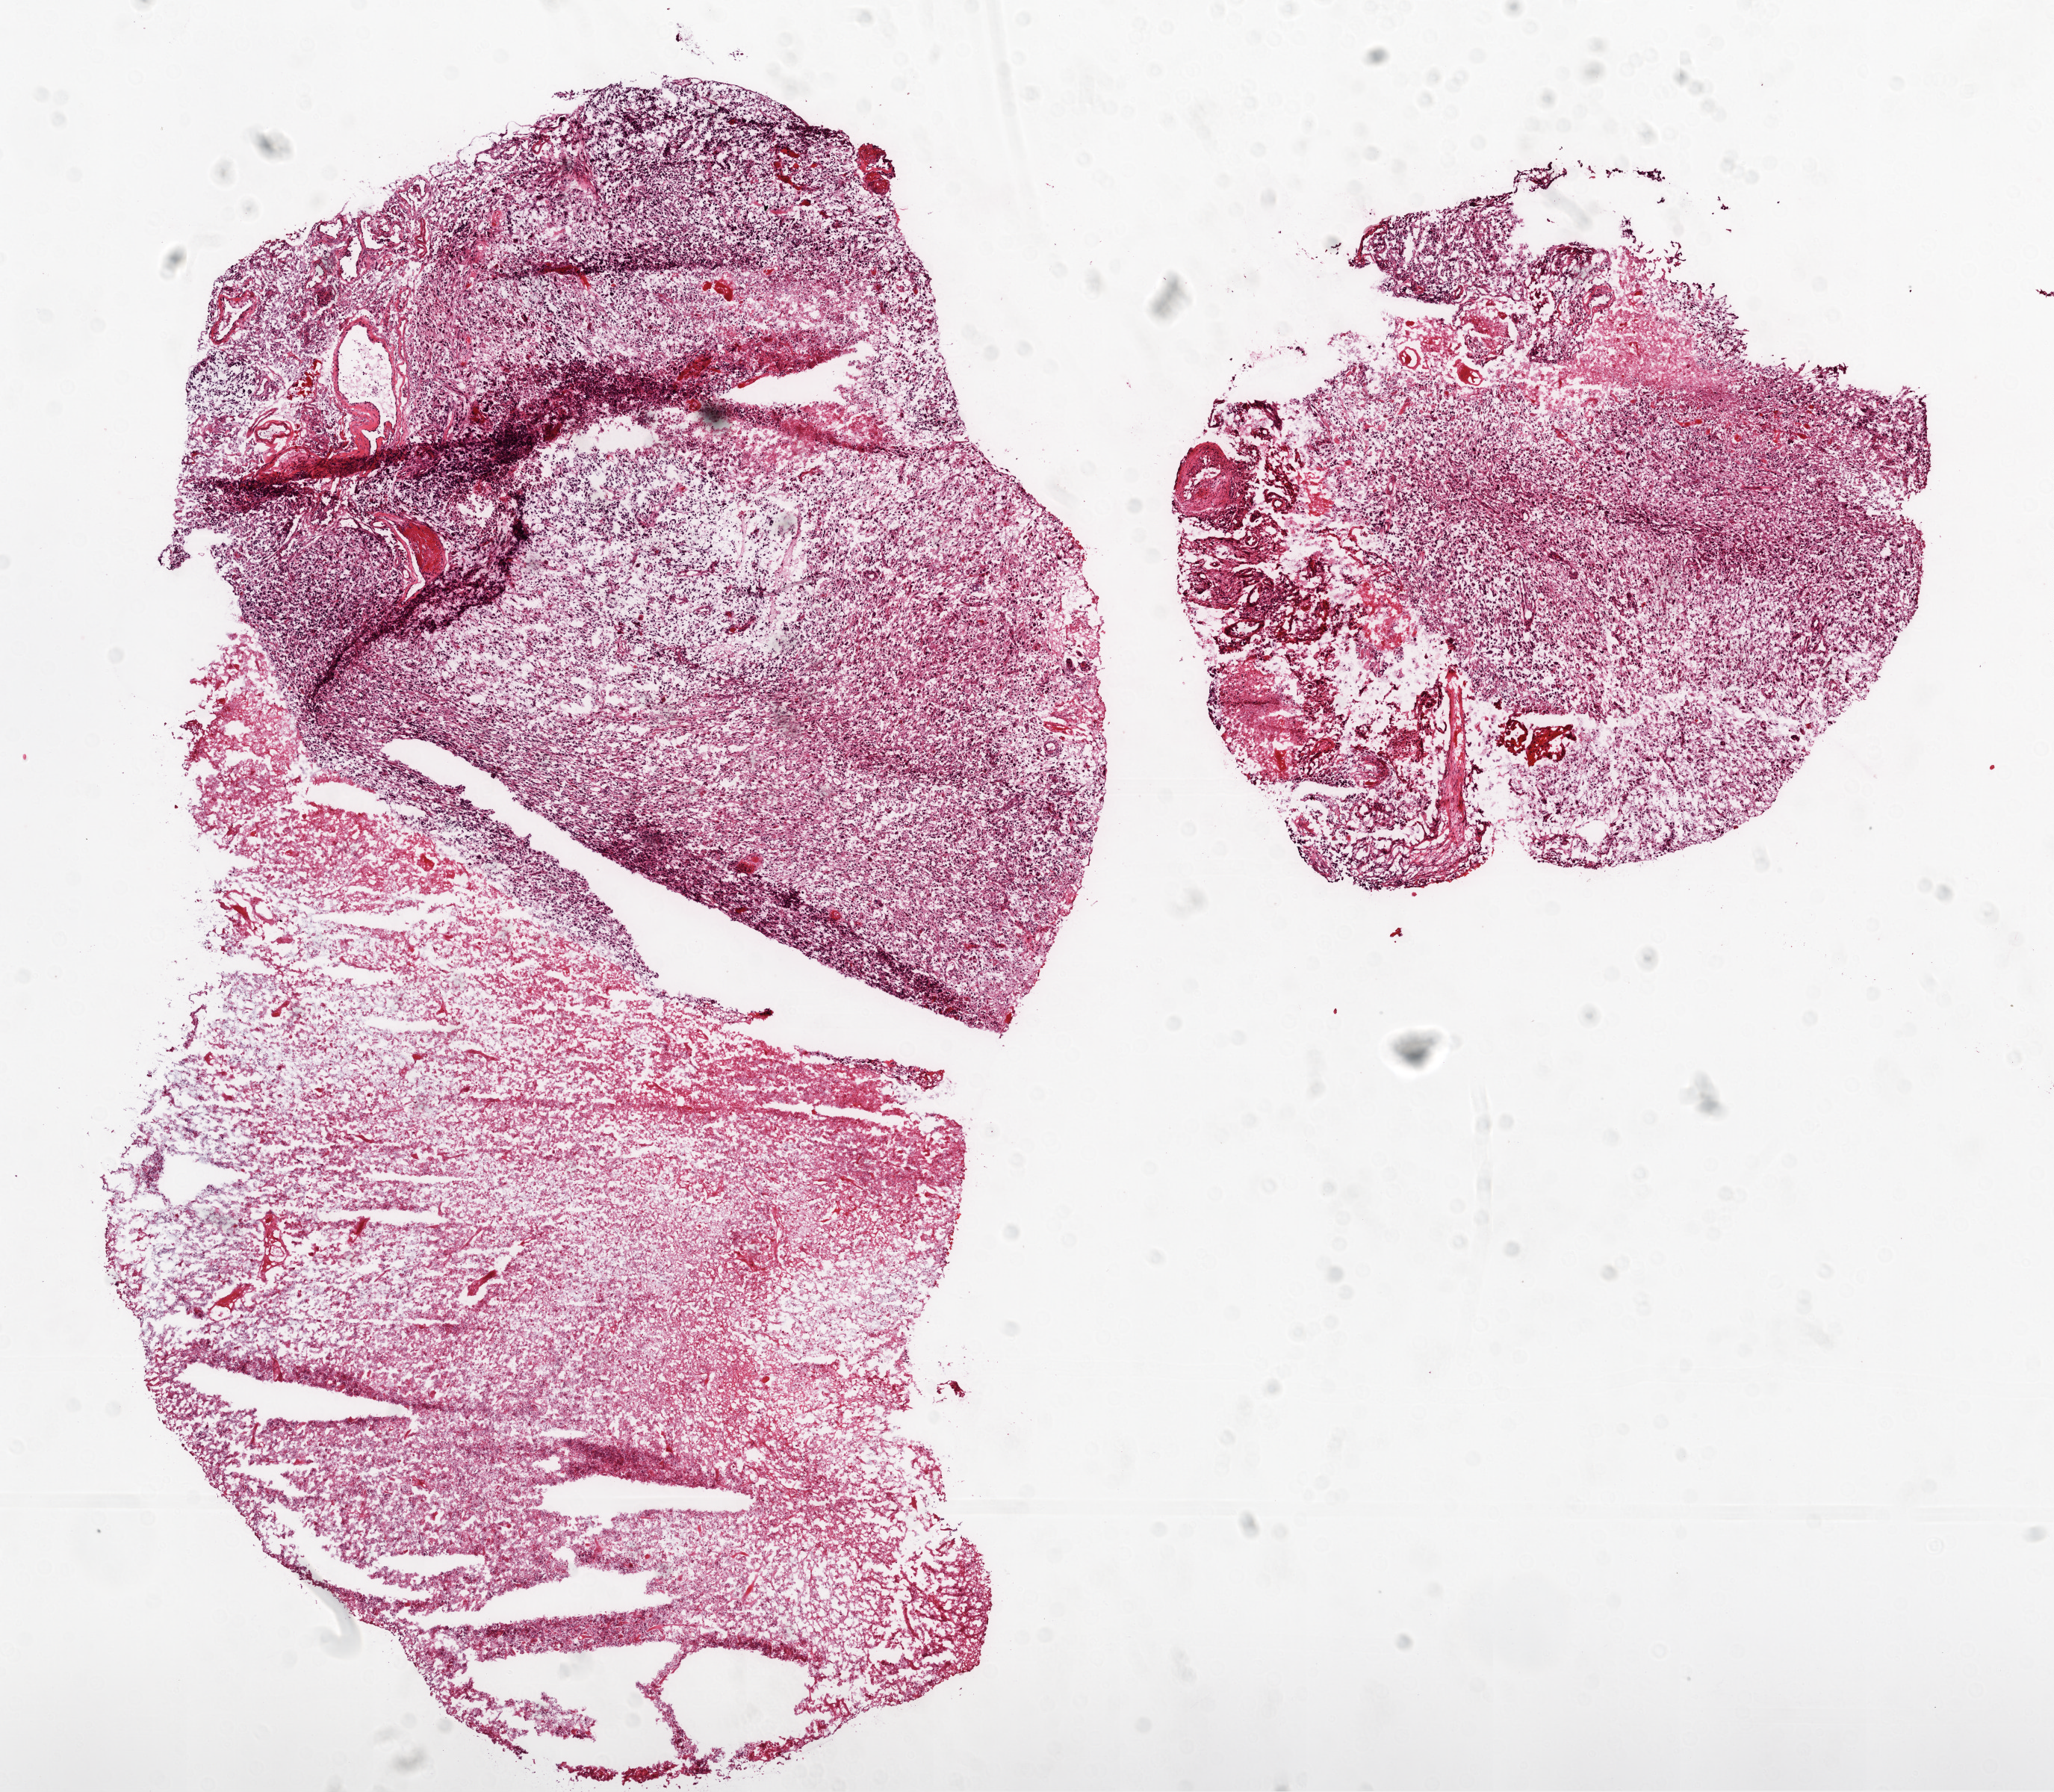
Digitized H&E tissue section (whole slide), shown as a low-resolution overview of the whole scanned area (about 11.0 x 9.6 mm, from a 20x scan), frozen section from the top of the tissue portion, primary tumour sample from the brain. Male, age 59 years at initial diagnosis. Slide review estimates, as recorded: tumour cells 50%, tumour nuclei 100%, normal cells 0%, stromal cells 0%, necrosis 50%.
Histologic diagnosis: Glioblastoma.